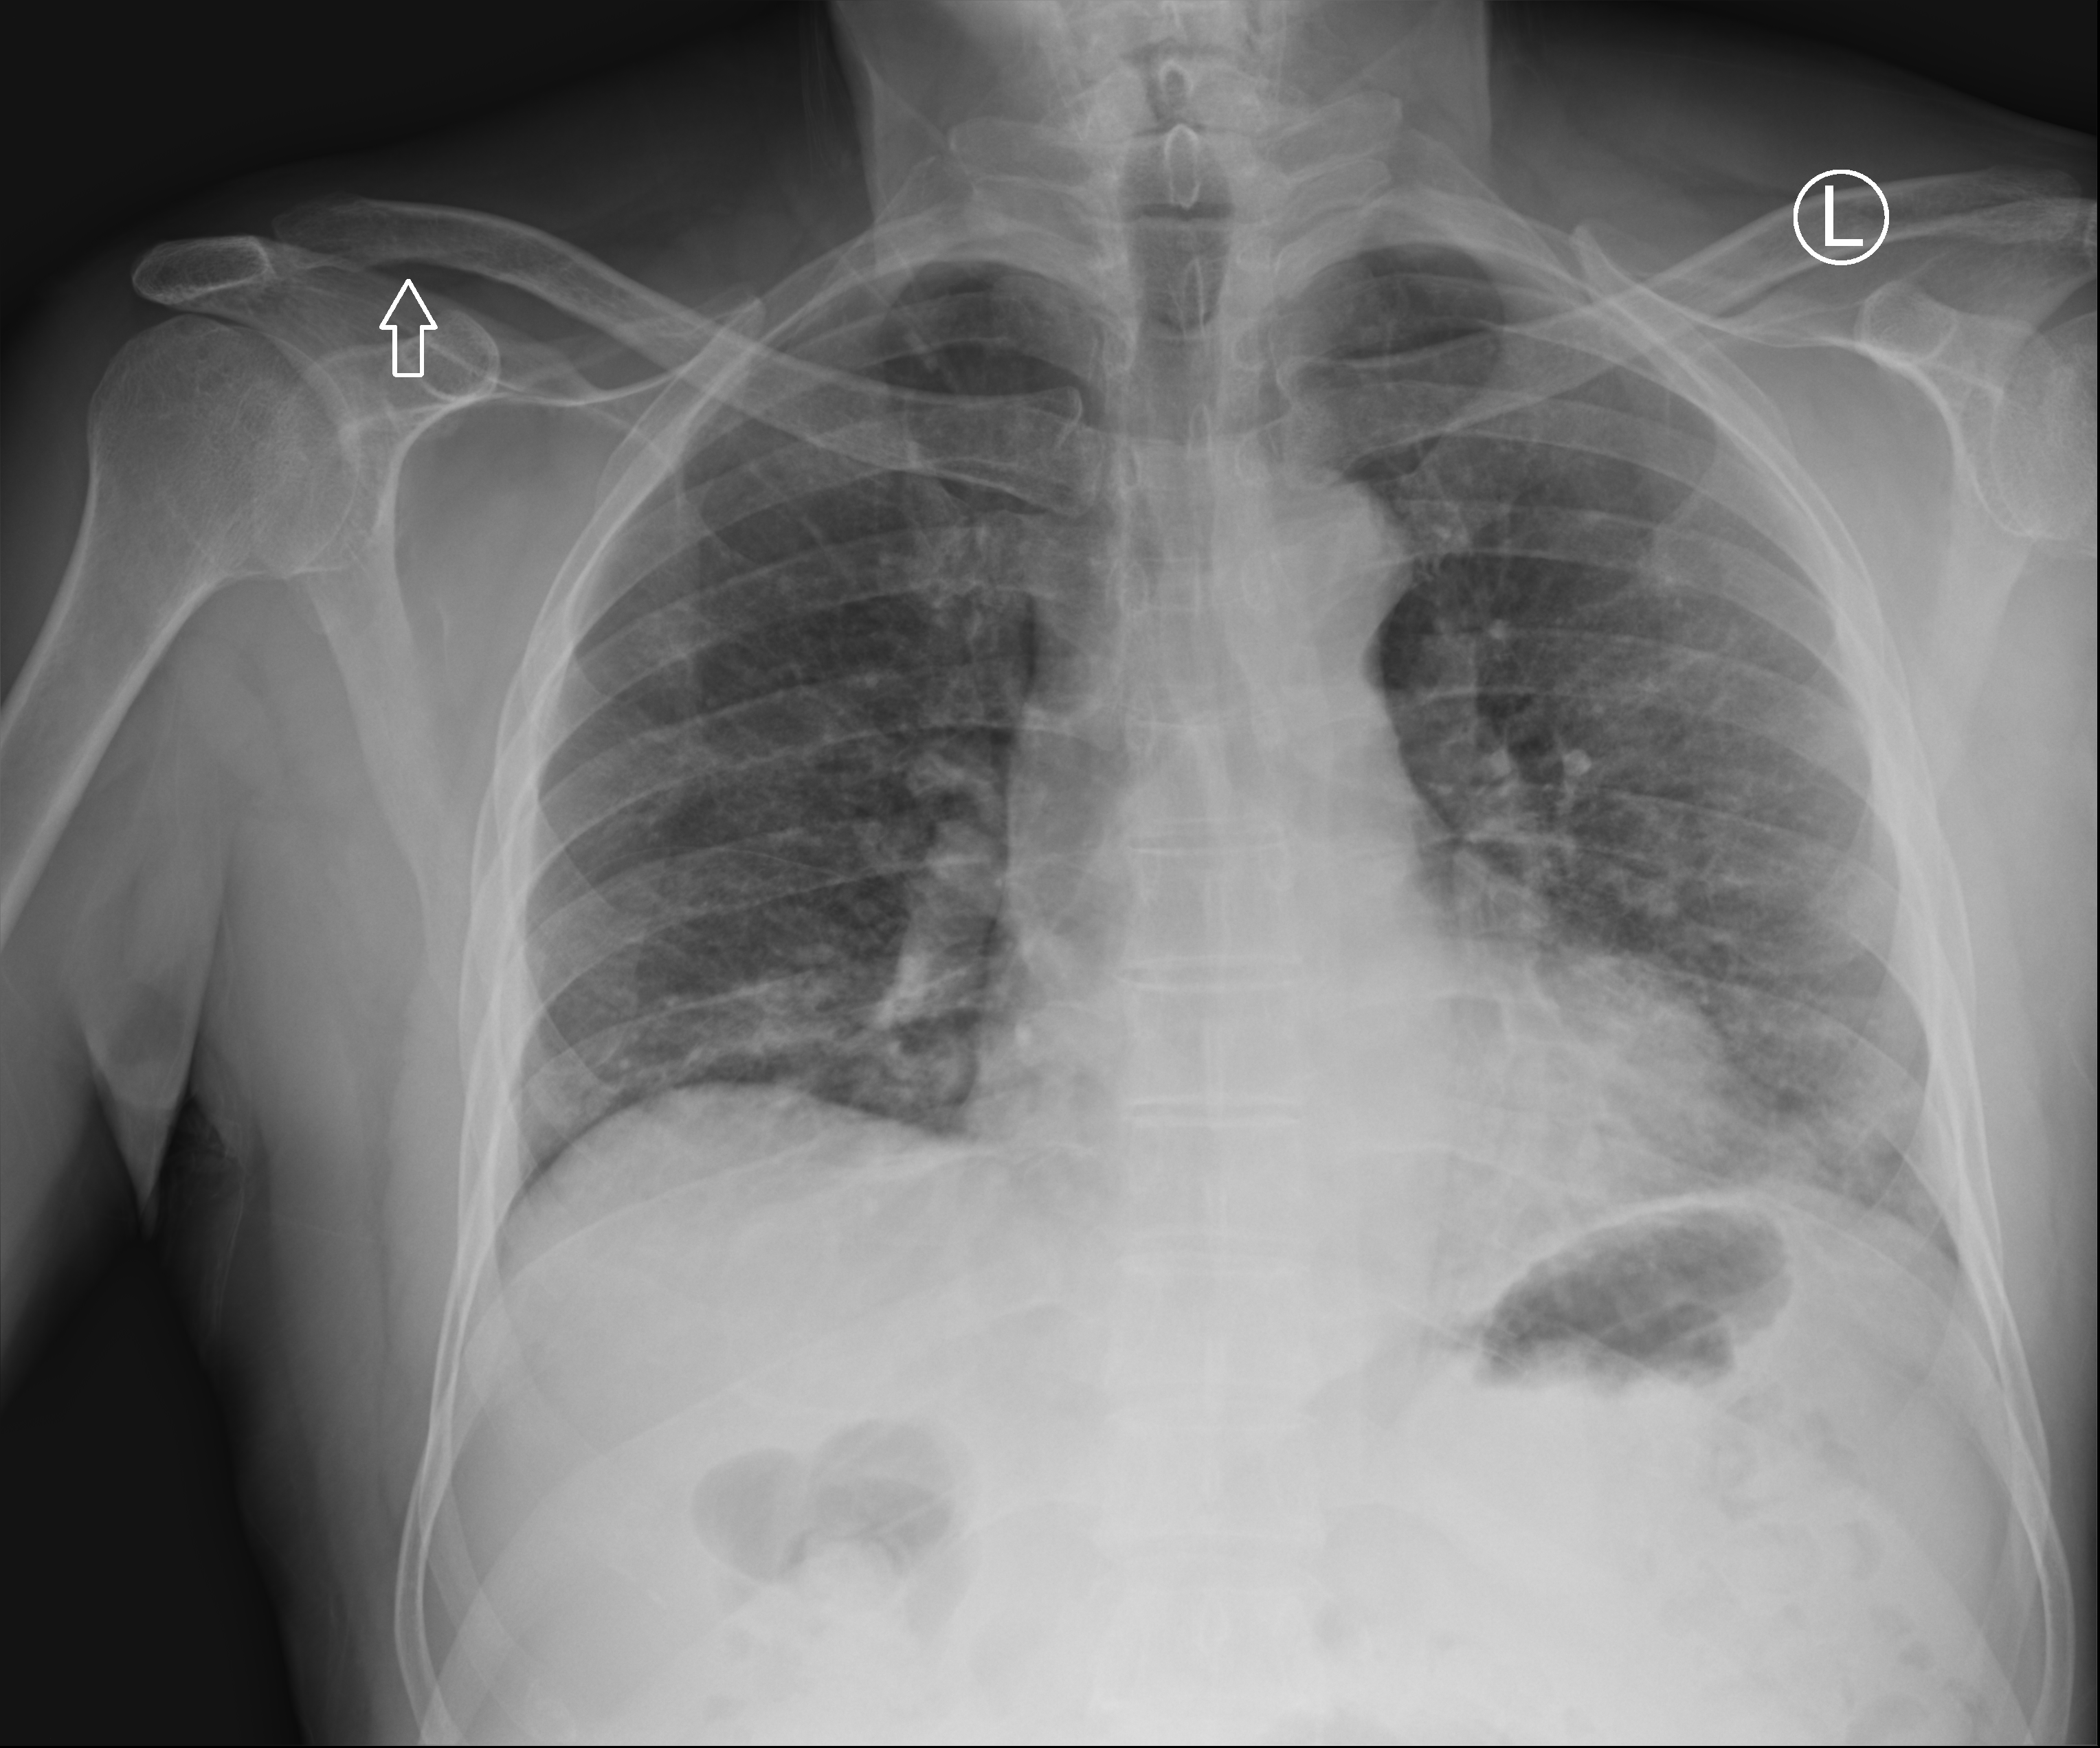
Chest radiograph (computed radiography). Male patient hospitalised with COVID-19, age 60–74 years.
From the hospital-stay record, not from the radiograph (when in the stay this image was taken is not recorded): admitted to intensive care during this hospital stay: no; mechanically ventilated during this hospital stay: no.